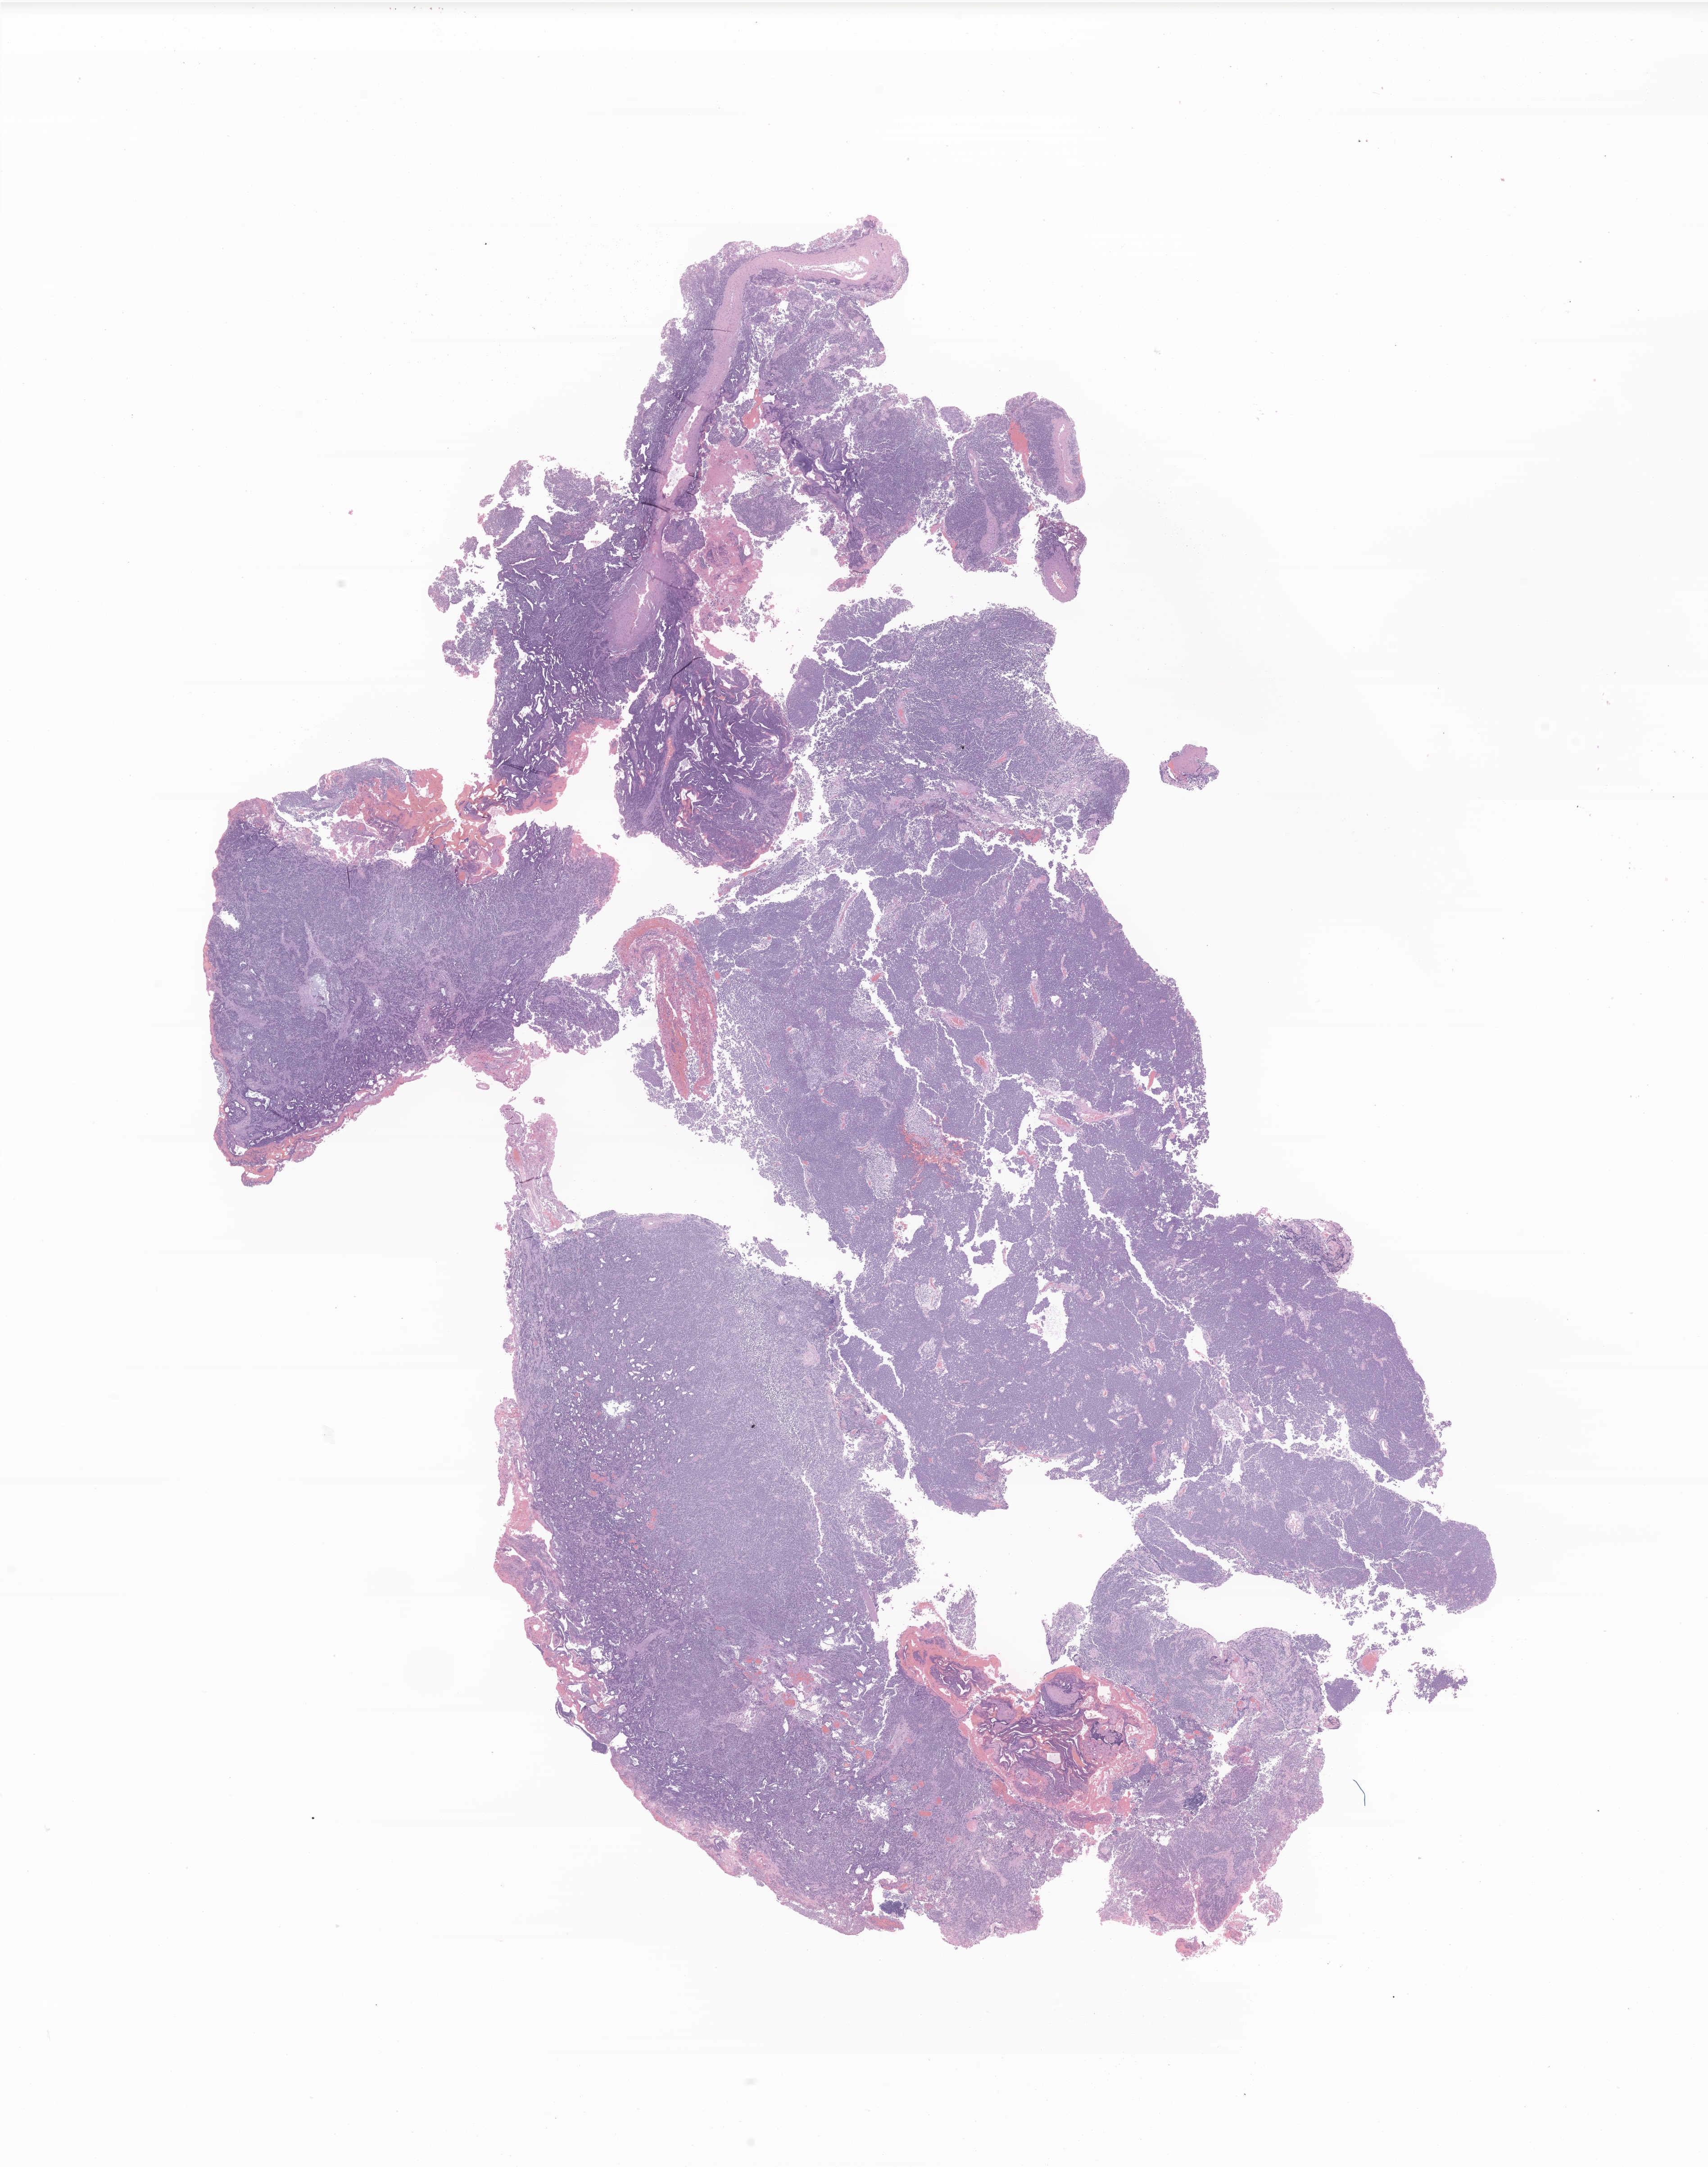
Haematoxylin and eosin whole-slide image of tumor tissue from the brain, shown as a low-resolution overview of the whole scanned area (about 16.0 x 20.3 mm); formalin-fixed, paraffin-embedded (FFPE) tissue. Patient: male, age 44 months (3 years 8 months).
Recorded diagnosis: Medulloblastoma, NOS.